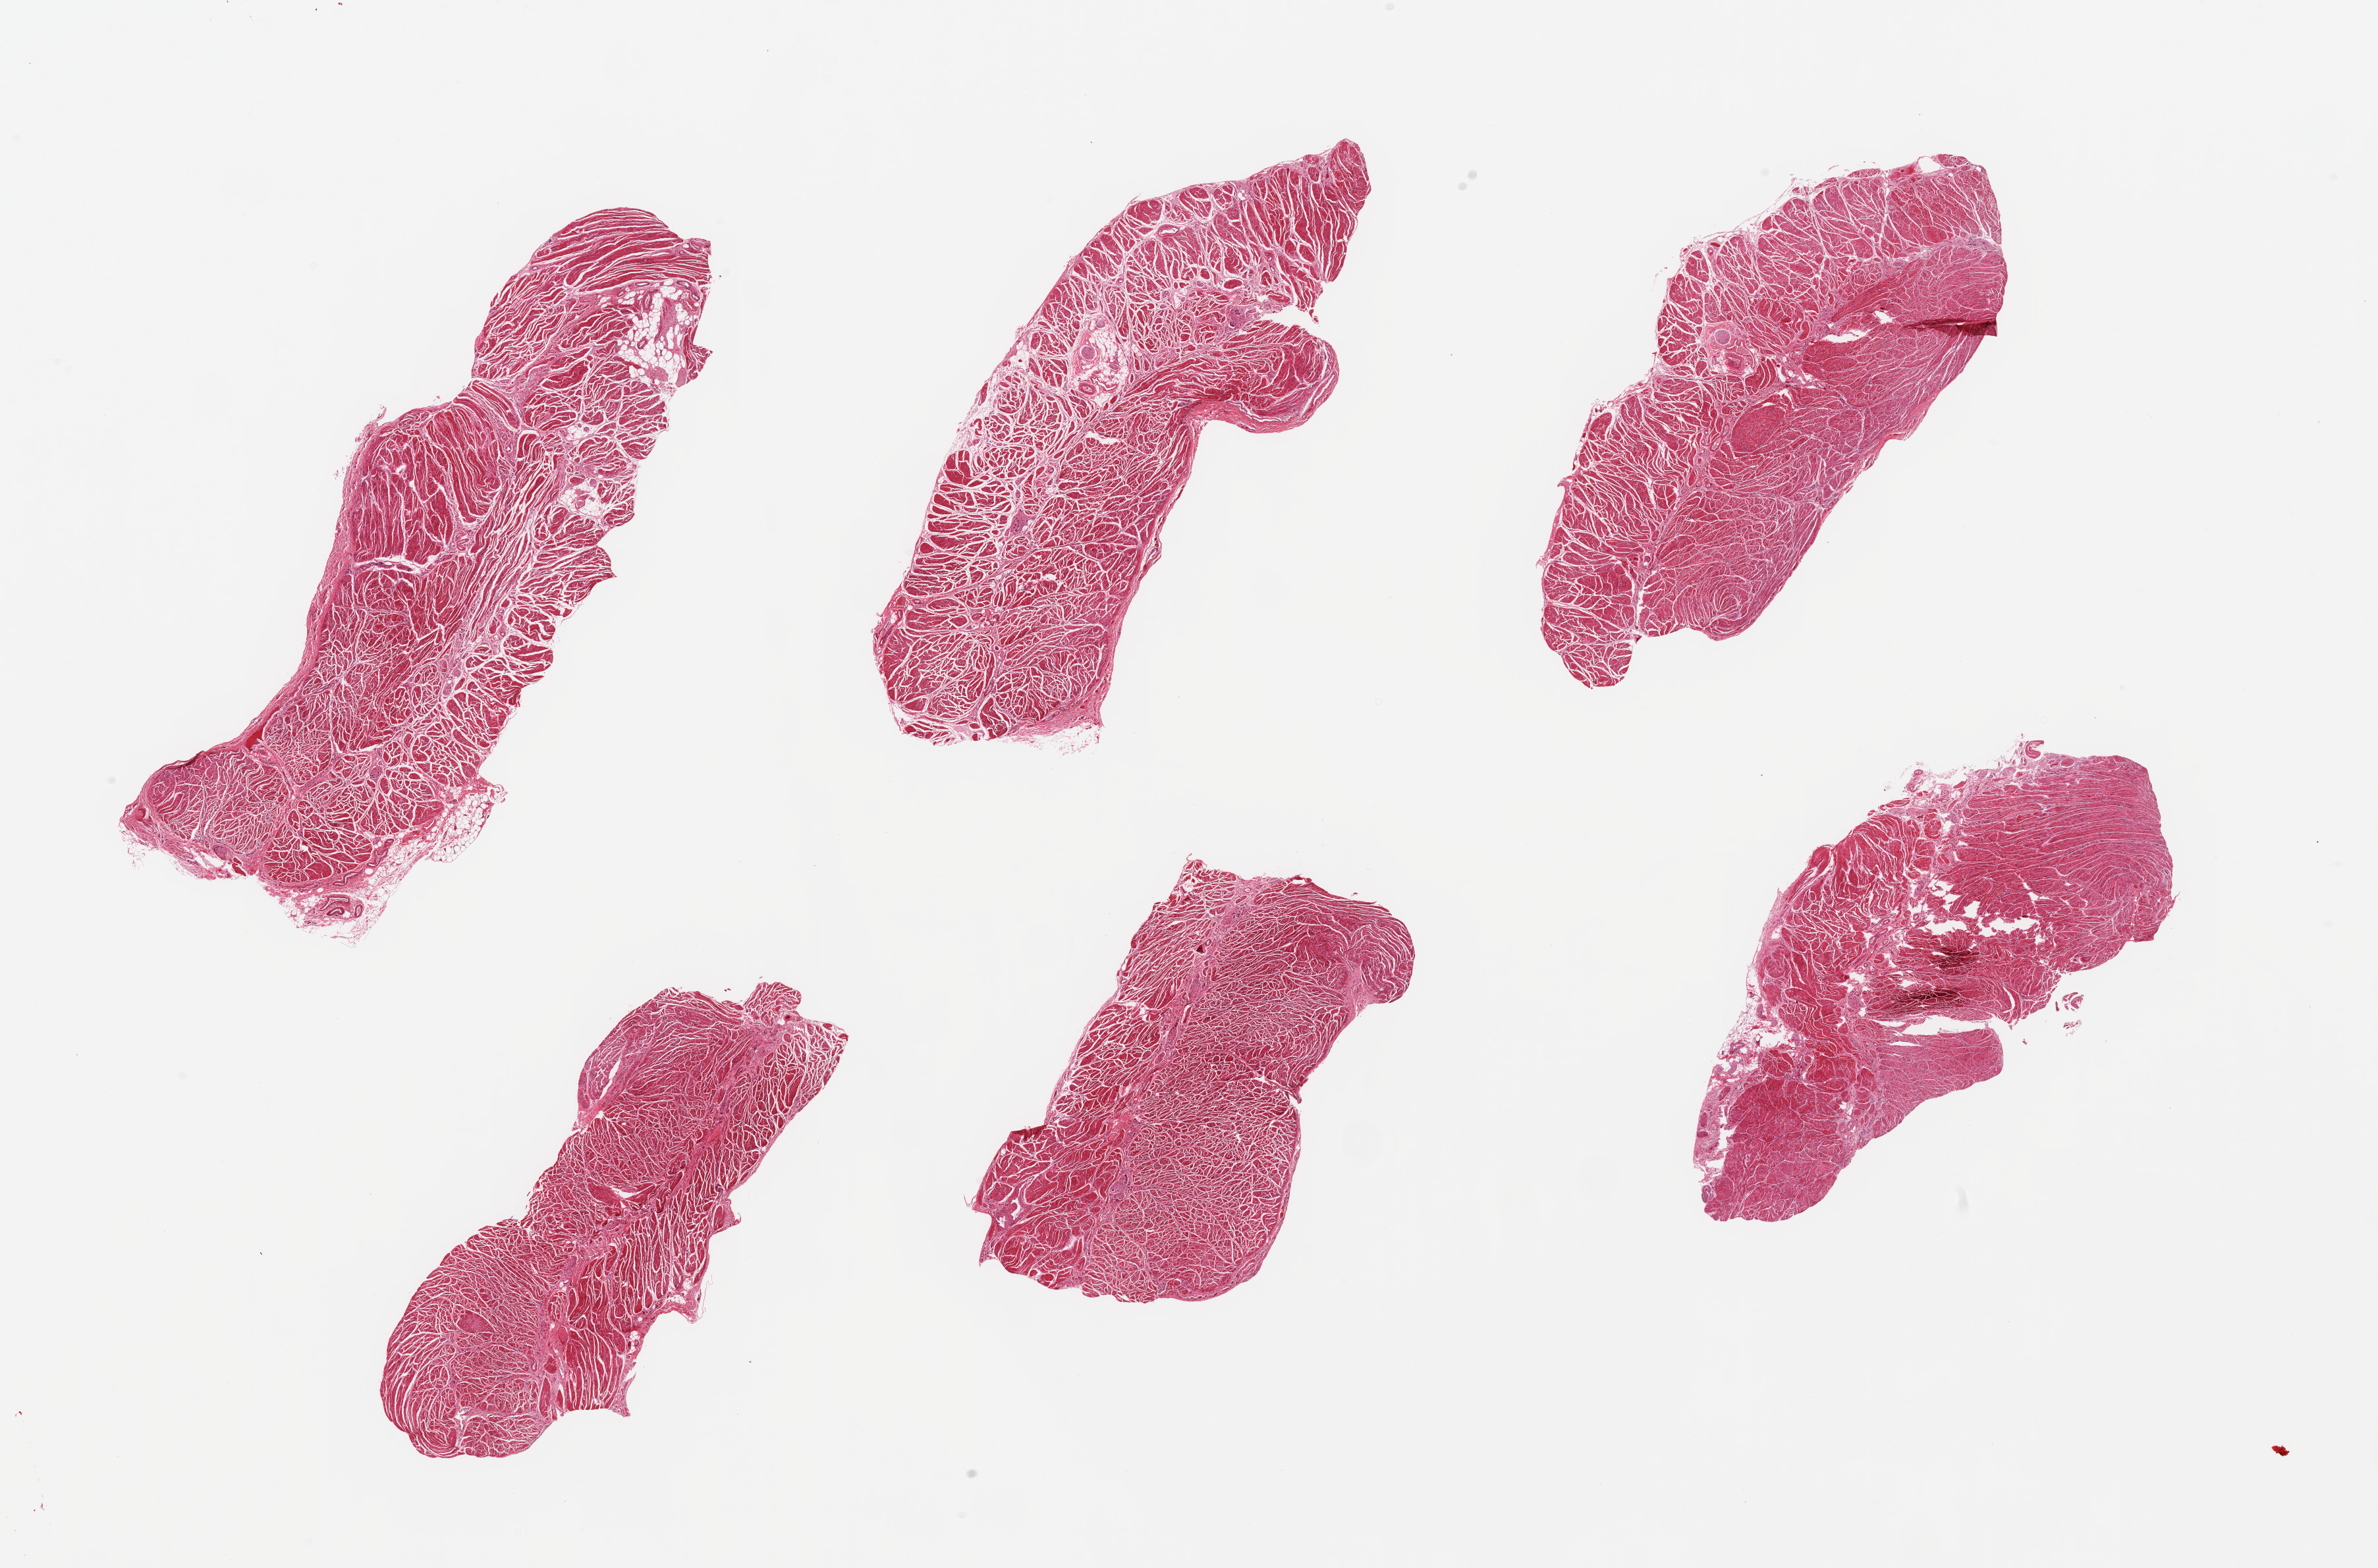
Digitized haematoxylin and eosin-stained section — whole scanned area (about 28.5 x 18.8 mm) shown as a low-resolution overview, PAXgene-fixed paraffin-embedded (PFPE) section, target tissue: gastroesophageal junction, donor tissue sample. Male donor.
- review note (as recorded): 6 pieces; well dissected muscularis